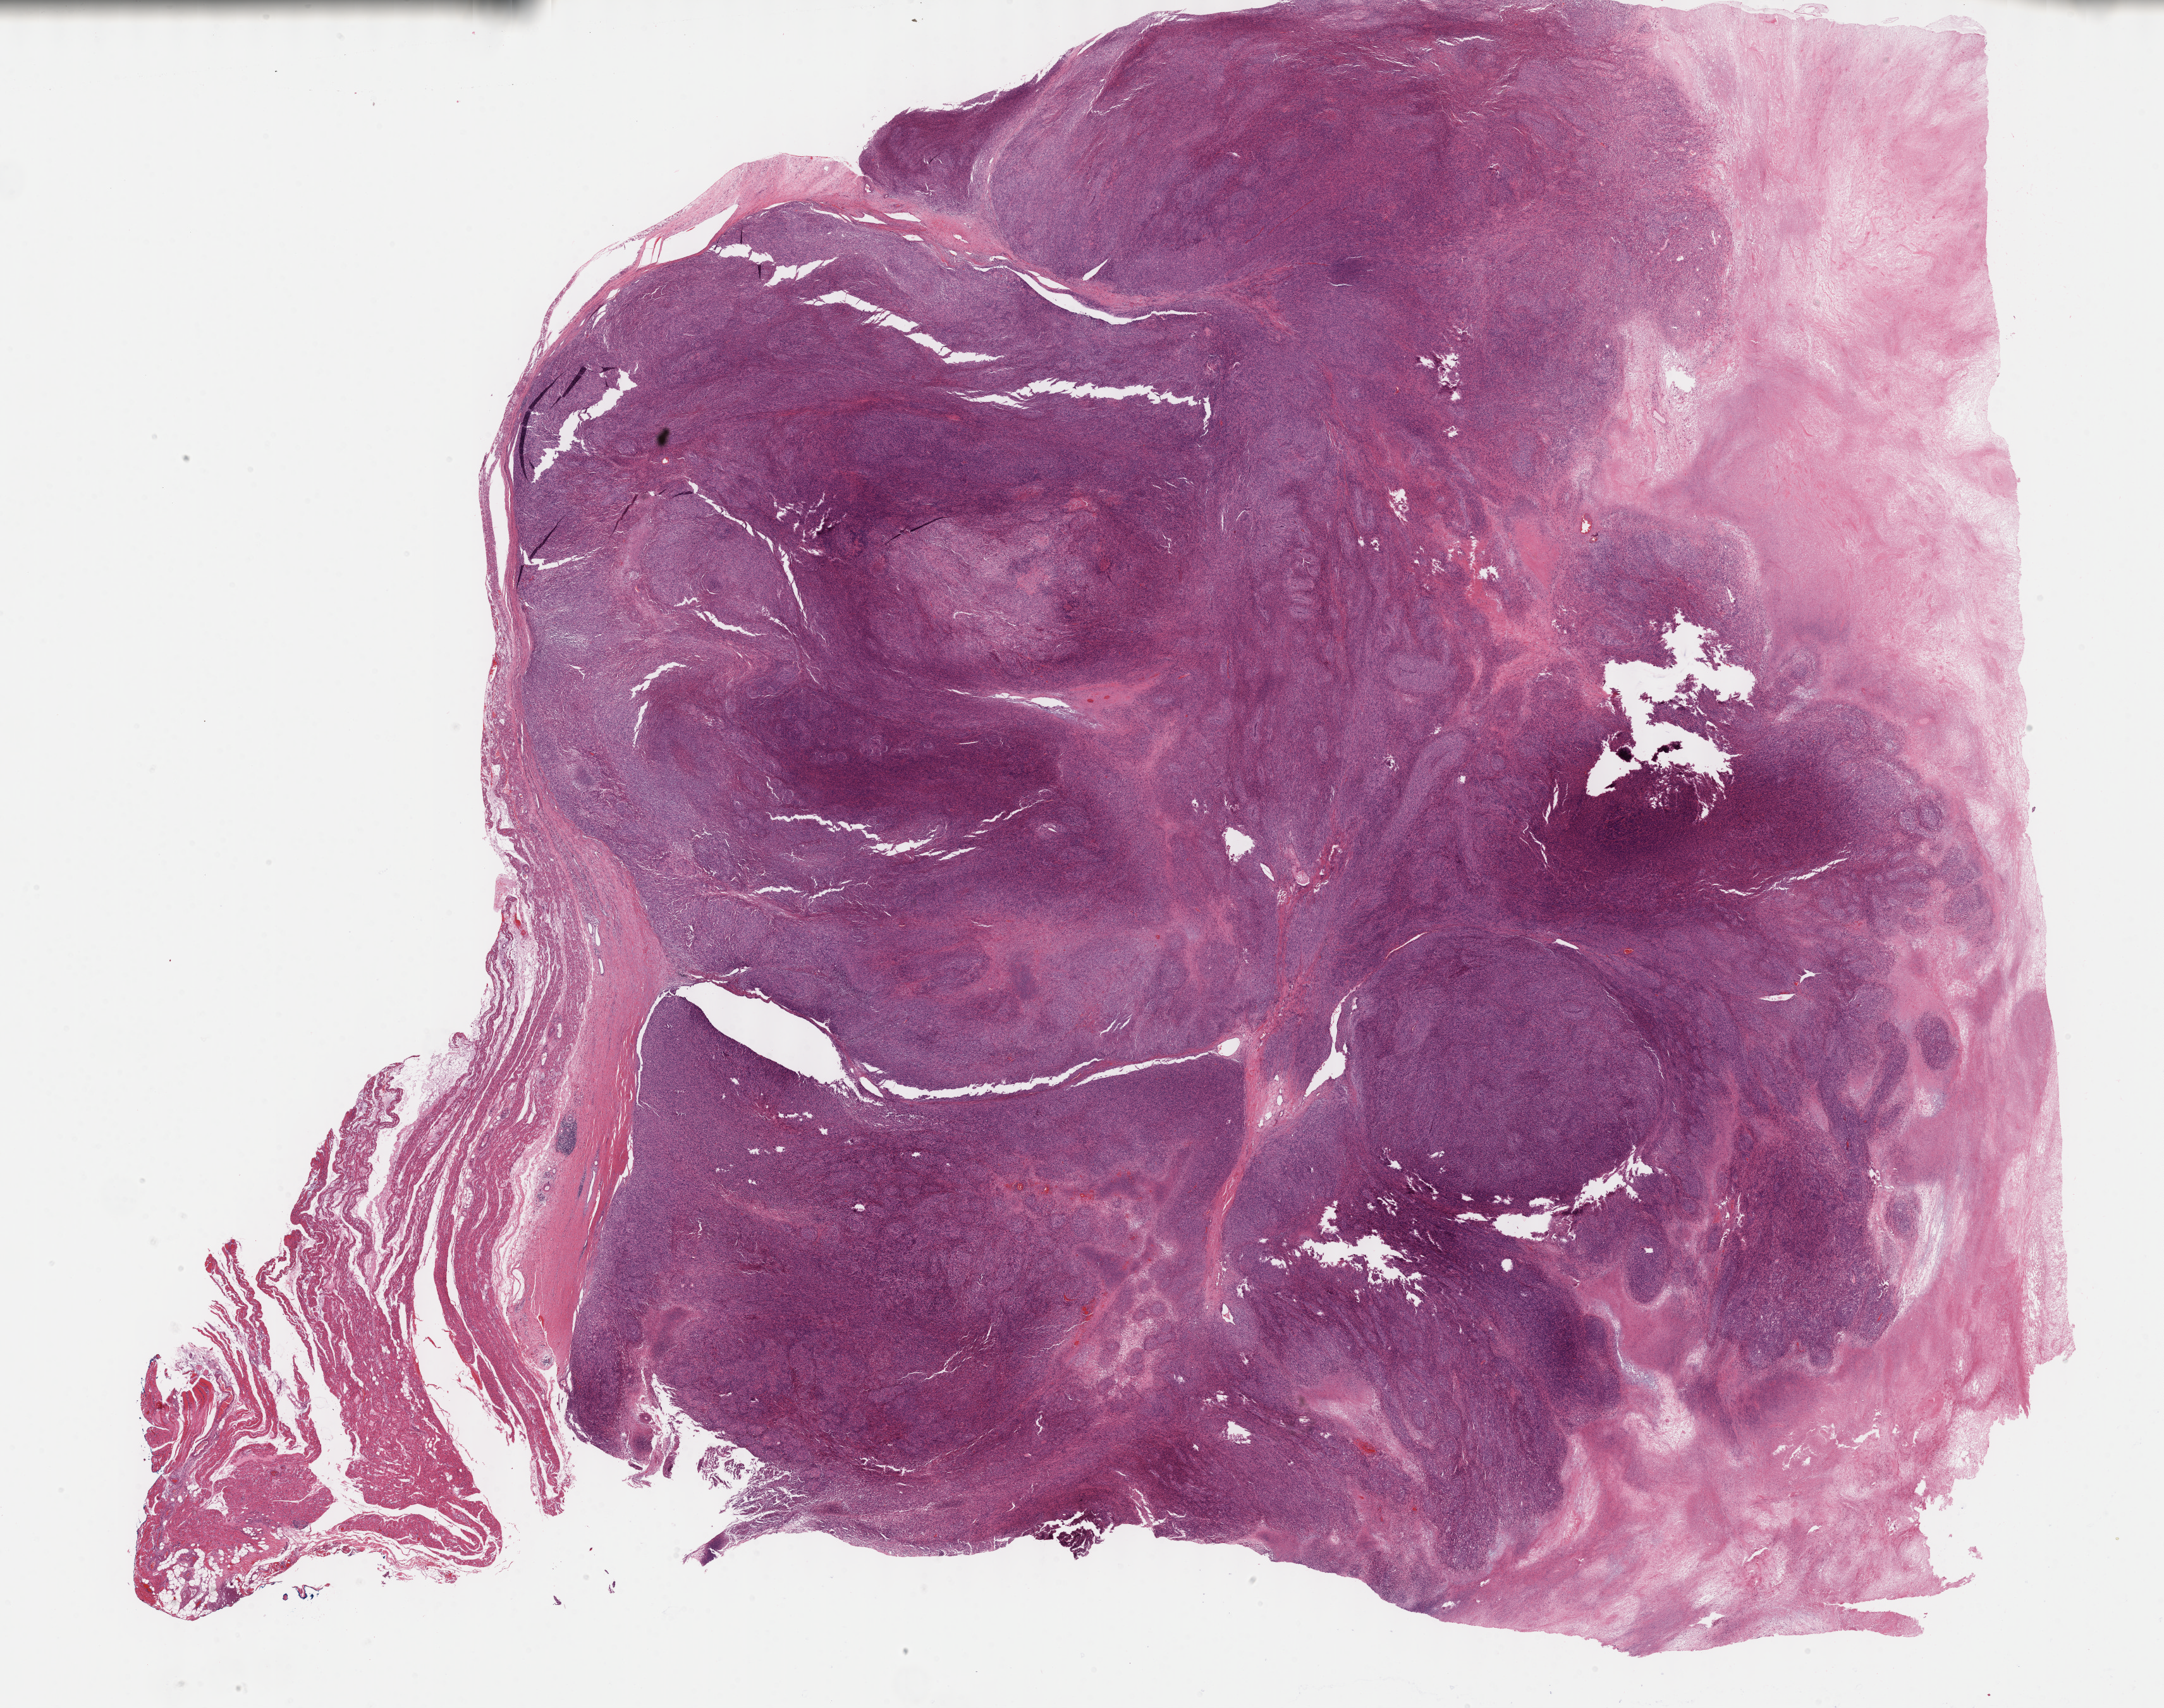
H&E-stained whole-slide image, whole scanned area (about 27.7 x 21.9 mm, slide scanned at 40x) shown as a low-resolution overview, formalin-fixed paraffin-embedded (FFPE) diagnostic section, retroperitoneum and peritoneum, primary tumour sample. Male, age 55 years at initial diagnosis.
Pathologic diagnosis: Undifferentiated sarcoma (retroperitoneum).